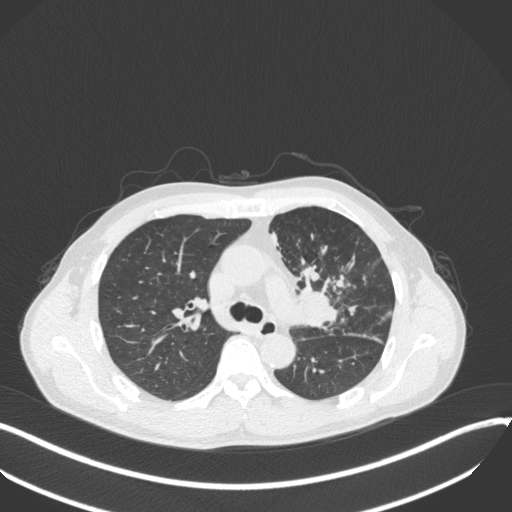
Chest CT, one axial slice; position 224 of 411 along the scan axis; reconstruction kernel B31f; 120 kVp; lung window (W 1500 / L -600 HU); 1 mm slice thickness; 512 × 512 image matrix, field of view 400 × 400 mm. Male patient, age 56 years. From the clinical record (not read from this slice): clinical TNM (as recorded): T2a N0 M0.
Outlined on this slice (rectangle marked by the reading radiologist):
- lung tumour (recorded histology: squamous cell carcinoma): bounding box <293,264,339,332> (left, top, right, bottom; pixels)